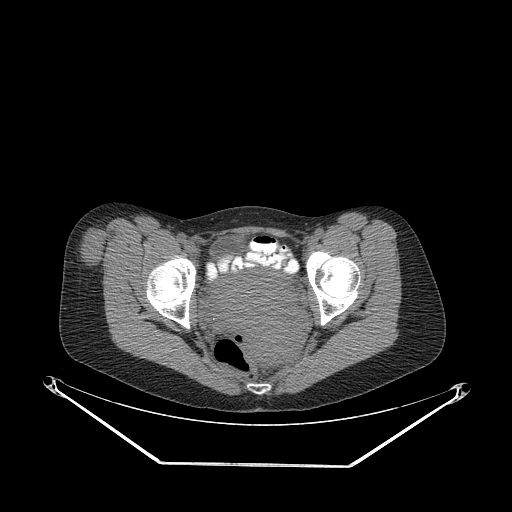
CT of an extremity soft-tissue mass (from a PET/CT study), one axial slice; position 70 of 267 along the scan axis; 140 kVp; soft-tissue window (W 400 / L 40 HU); 512 × 512 image matrix, field of view 500 × 500 mm. Female patient. From the clinical record (not read from this slice): histological type: synovial sarcoma; grade: intermediate; site of the primary tumour: right thigh.
Annotated regions visible in this slice (expert contour drawn on MRI and transferred to this co-registered scan by the dataset authors):
- gross tumour volume including surrounding oedema: bounding box (x1, y1, x2, y2) in pixels: (80, 228, 111, 268)
- gross tumour volume (mass): (80, 231, 106, 268)